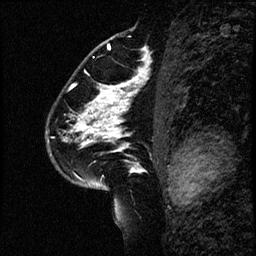
Breast MRI (dynamic contrast-enhanced), one sagittal slice. Position 39 of 60 along the scan axis. Dynamic contrast-enhanced study with each time point stored as its own series, time point 2 of 4 at this slice position (early post-contrast, ordered by acquisition time). 1.5 T. TE 4.2 ms, TR 17.6 ms. 2 mm slice thickness. 256 × 256 image matrix, field of view 200 × 200 mm. Patient: female, 43 years. Case-level facts recorded for this patient, not image findings: setting: breast cancer imaged before/during neoadjuvant chemotherapy.
Outlined on this slice (semi-automatic segmentation, software-assisted and operator-edited):
- analysis volume of interest (the breast-tissue region the enhancement analysis was run in; not a lesion): bounding box <49,56,169,191> (left, top, right, bottom; pixels)
- tumour enhancement mask (voxels above the 100 % enhancement threshold inside the analysis volume of interest): <70,83,131,182>